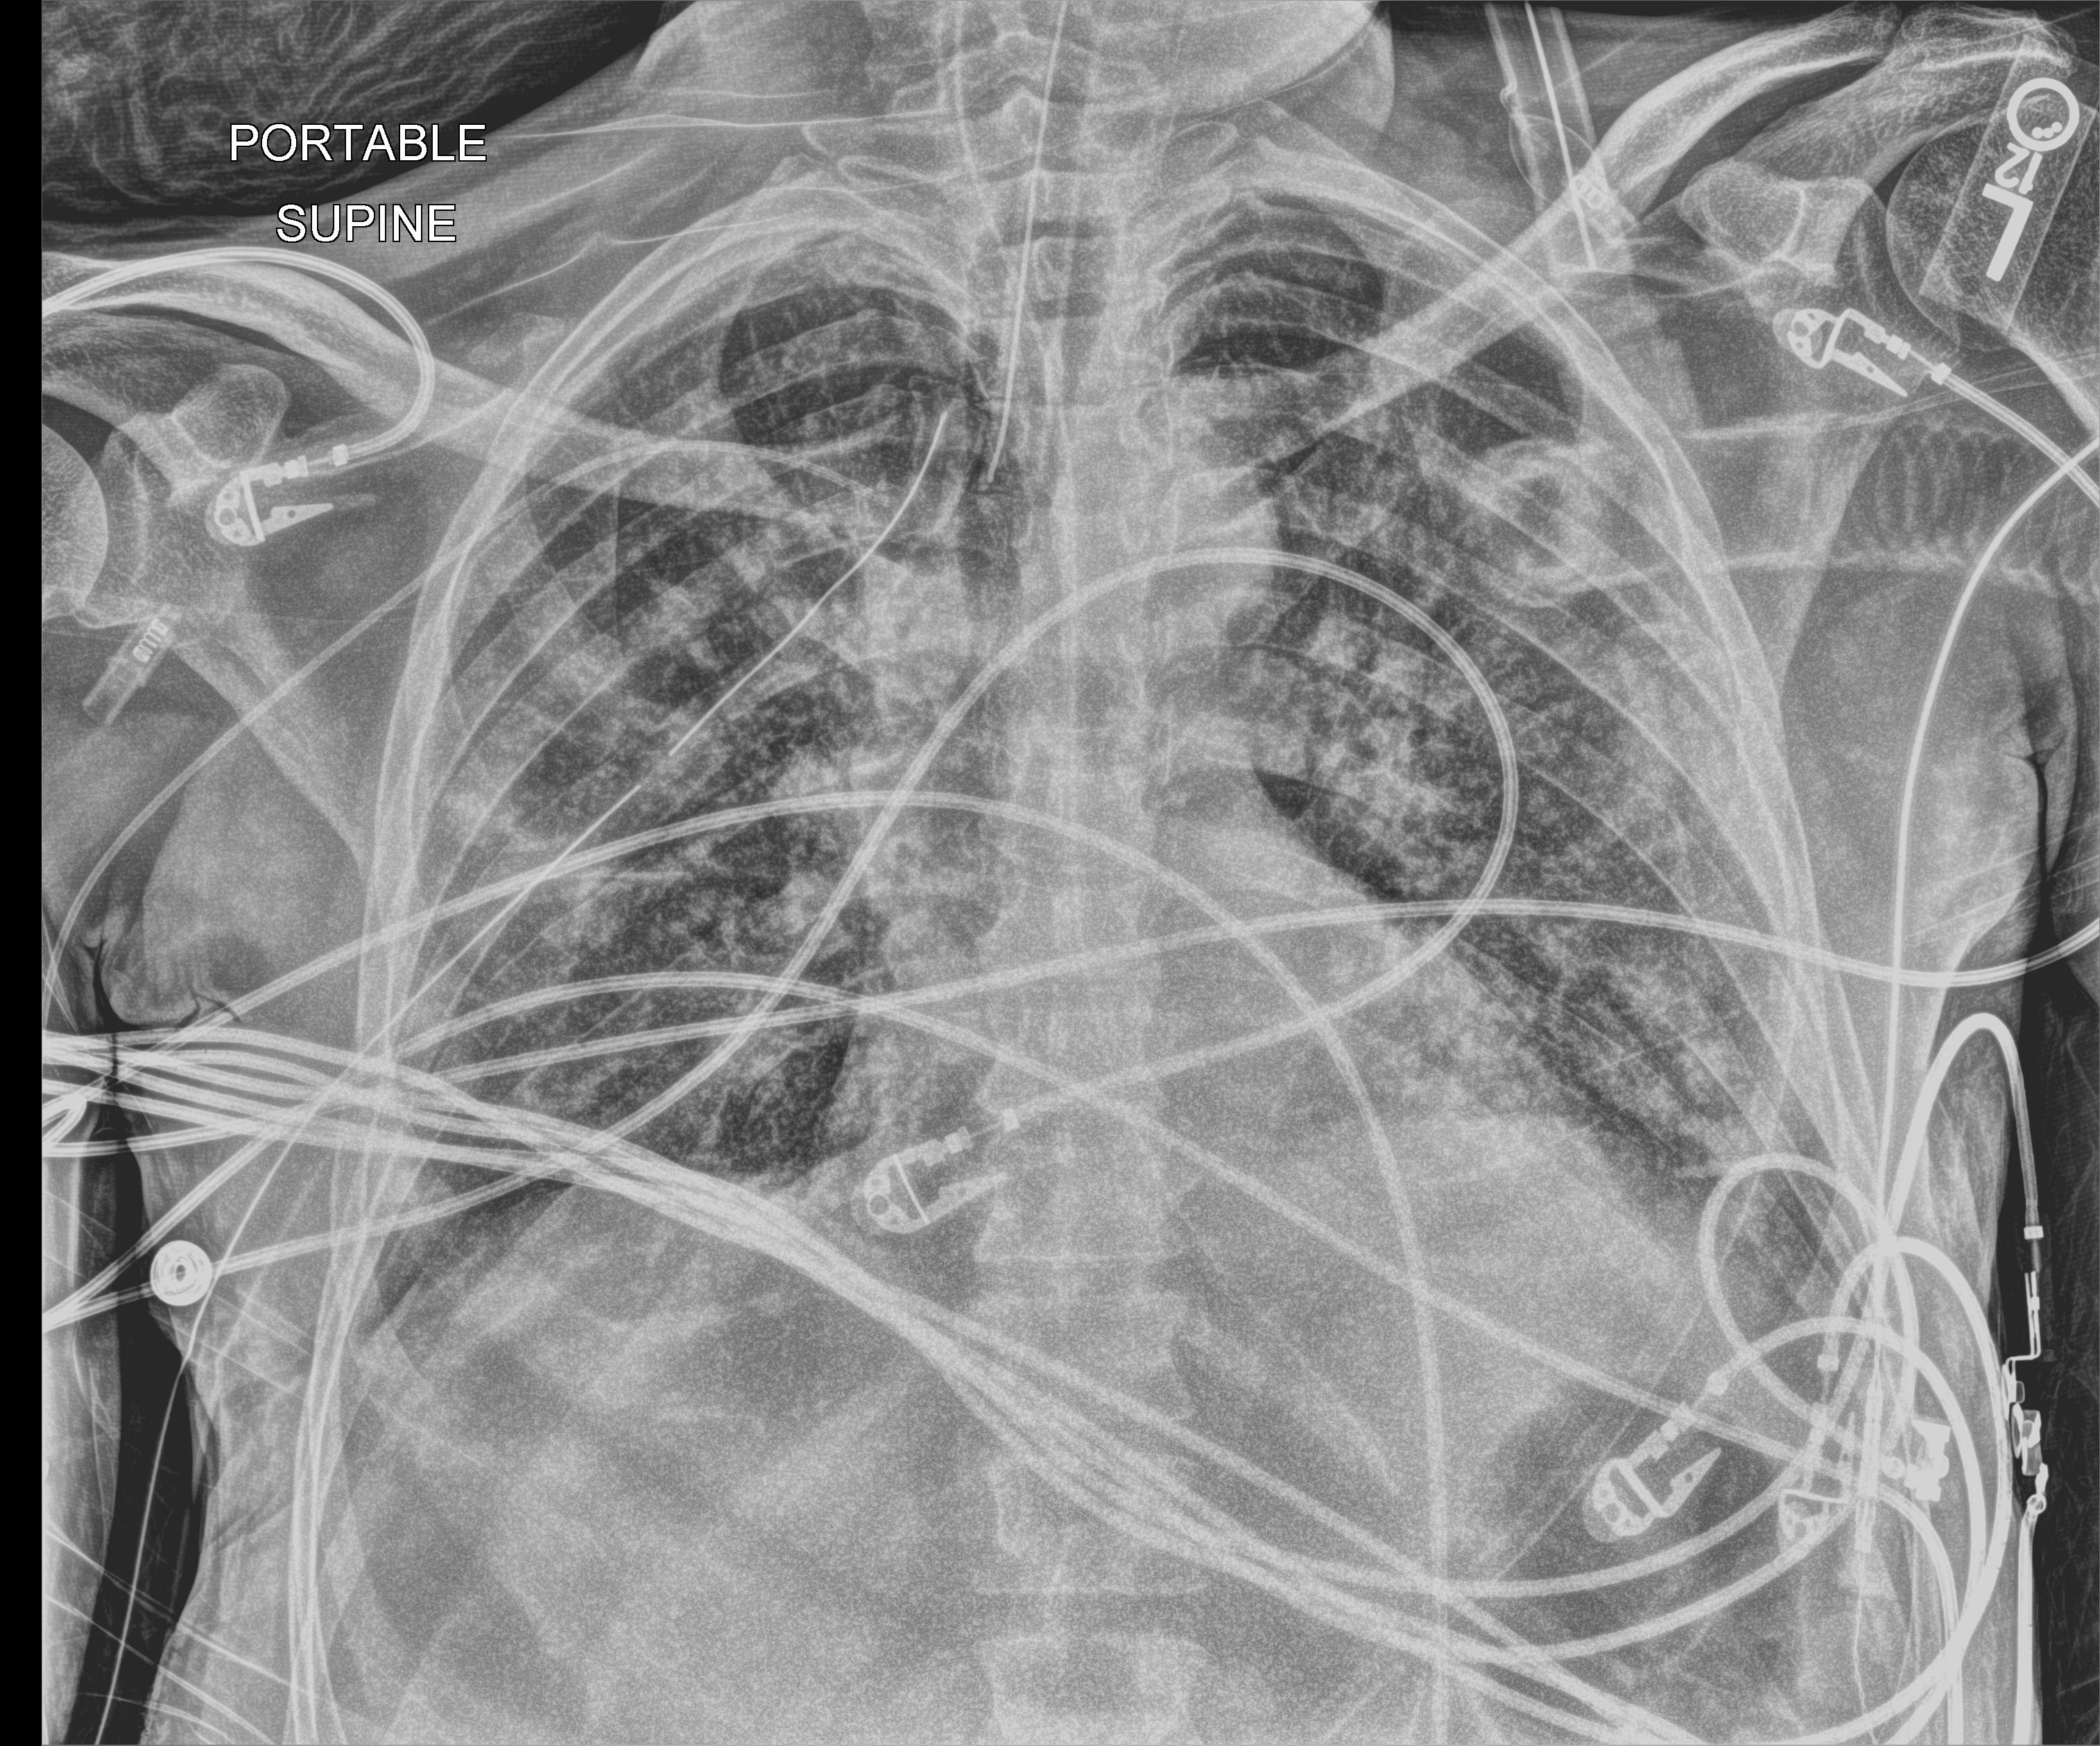
Bedside chest radiograph (computed radiography), anteroposterior (AP) projection. Patient hospitalised with COVID-19; male, aged 18–59 years.
Hospital-stay facts (about this admission, not read from this image; timing relative to this image not recorded): hypertension (admission record): no.